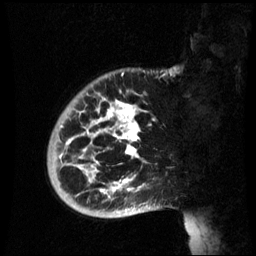
Breast MRI (dynamic contrast-enhanced), one sagittal slice. Dynamic contrast-enhanced series, image 2 of 3 at this slice position (ordered by acquisition). 1.5 T. TE 4.2 ms, TR 8.9 ms. 2.6 mm slice thickness. 256 × 256 image matrix, field of view 220 × 220 mm. Female patient, age 35 years. Case-level facts recorded for this patient, not image findings: setting: breast cancer imaged before/during neoadjuvant chemotherapy; receptor status: HR-positive, HER2-negative.
Structures marked on this image (semi-automatic segmentation, software-assisted and operator-edited):
- analysis volume of interest (the breast-tissue region the enhancement analysis was run in; not a lesion): bounding box <47,74,162,219> (left, top, right, bottom; pixels)
- tumour enhancement mask (voxels above the 70 % enhancement threshold inside the analysis volume of interest): <67,100,141,199>